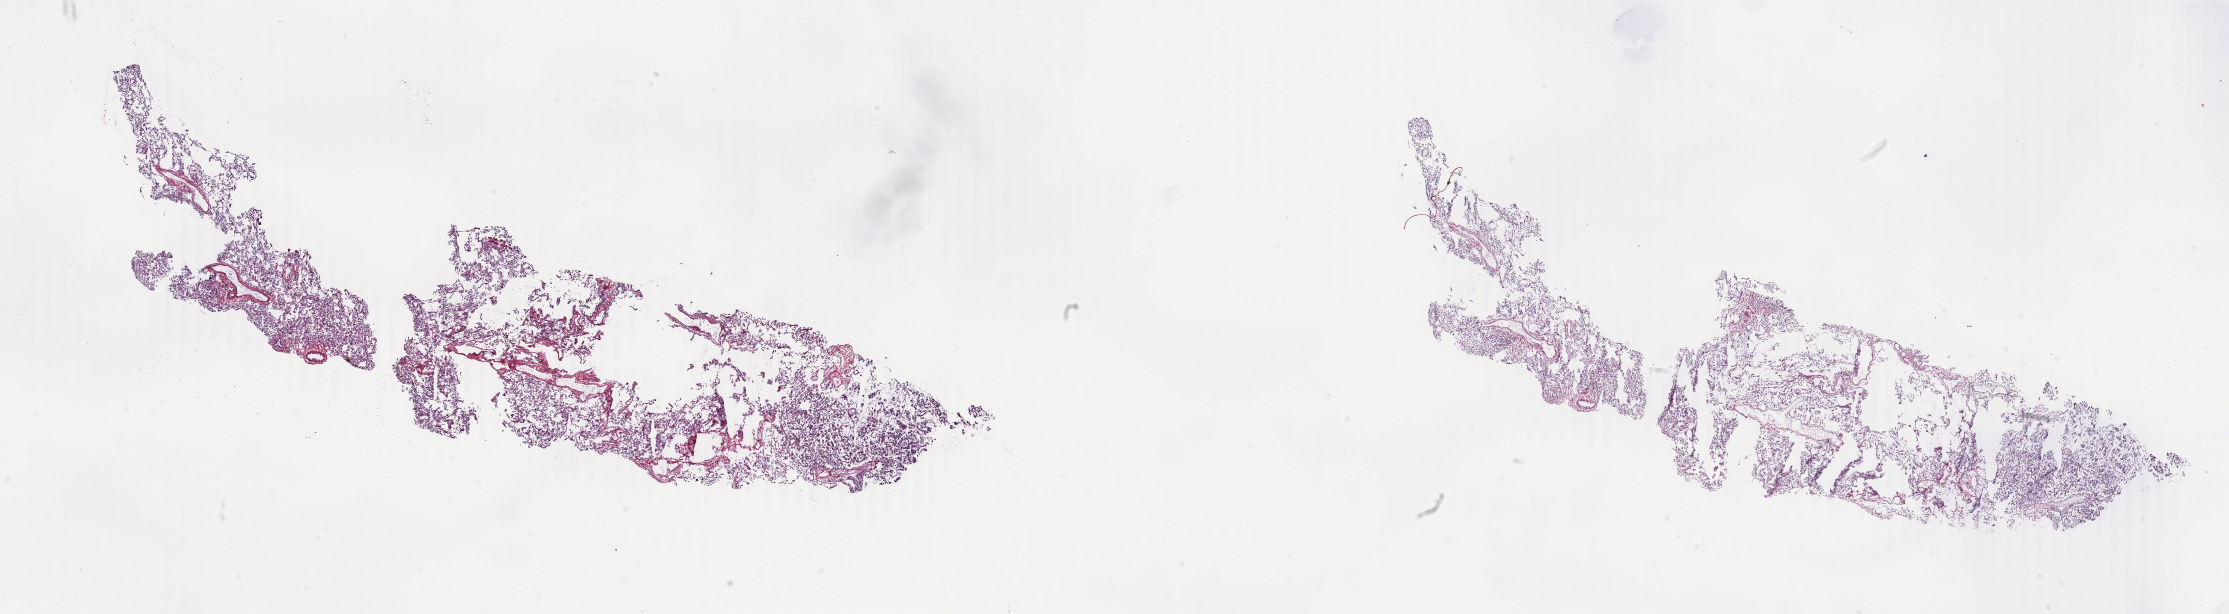
Whole-slide histology image, H&E, shown as a low-resolution overview of the whole scanned area (about 35.5 x 9.8 mm, slide scanned at 40x), frozen section from the top of the tissue portion, primary tumour sample from the lung. Male, age 64 years at initial diagnosis. Composition of this section per pathologist review: tumour cells 65%, tumour nuclei 65%.
Diagnosis: Papillary adenocarcinoma, NOS (lower lobe, lung).